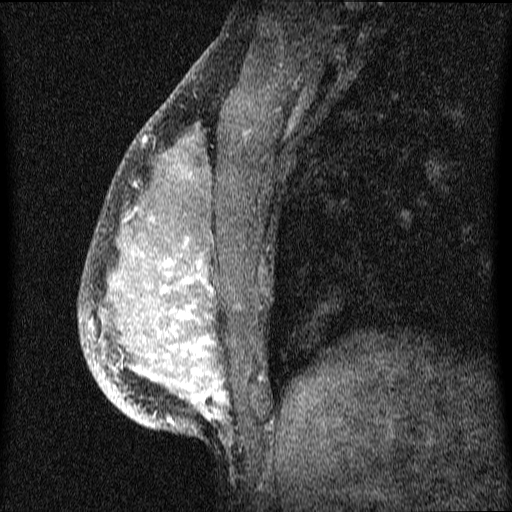
Breast MRI (dynamic contrast-enhanced), one sagittal slice. Slice 24 of 64 in the series (ordered by position). Dynamic contrast-enhanced series, image 2 of 4 at this slice position (ordered by acquisition). 1.5 T. TE 4.2 ms, TR 9.1 ms. 2 mm slice thickness. 512 × 512 image matrix. Patient: female, 33 years.
Outlined on this slice (semi-automatic segmentation, software-assisted and operator-edited):
- analysis volume of interest (the breast-tissue region the enhancement analysis was run in; not a lesion): bounding box <79,151,336,457> (left, top, right, bottom; pixels)
- tumour enhancement mask (voxels above the 70 % enhancement threshold inside the analysis volume of interest): <92,208,227,423>